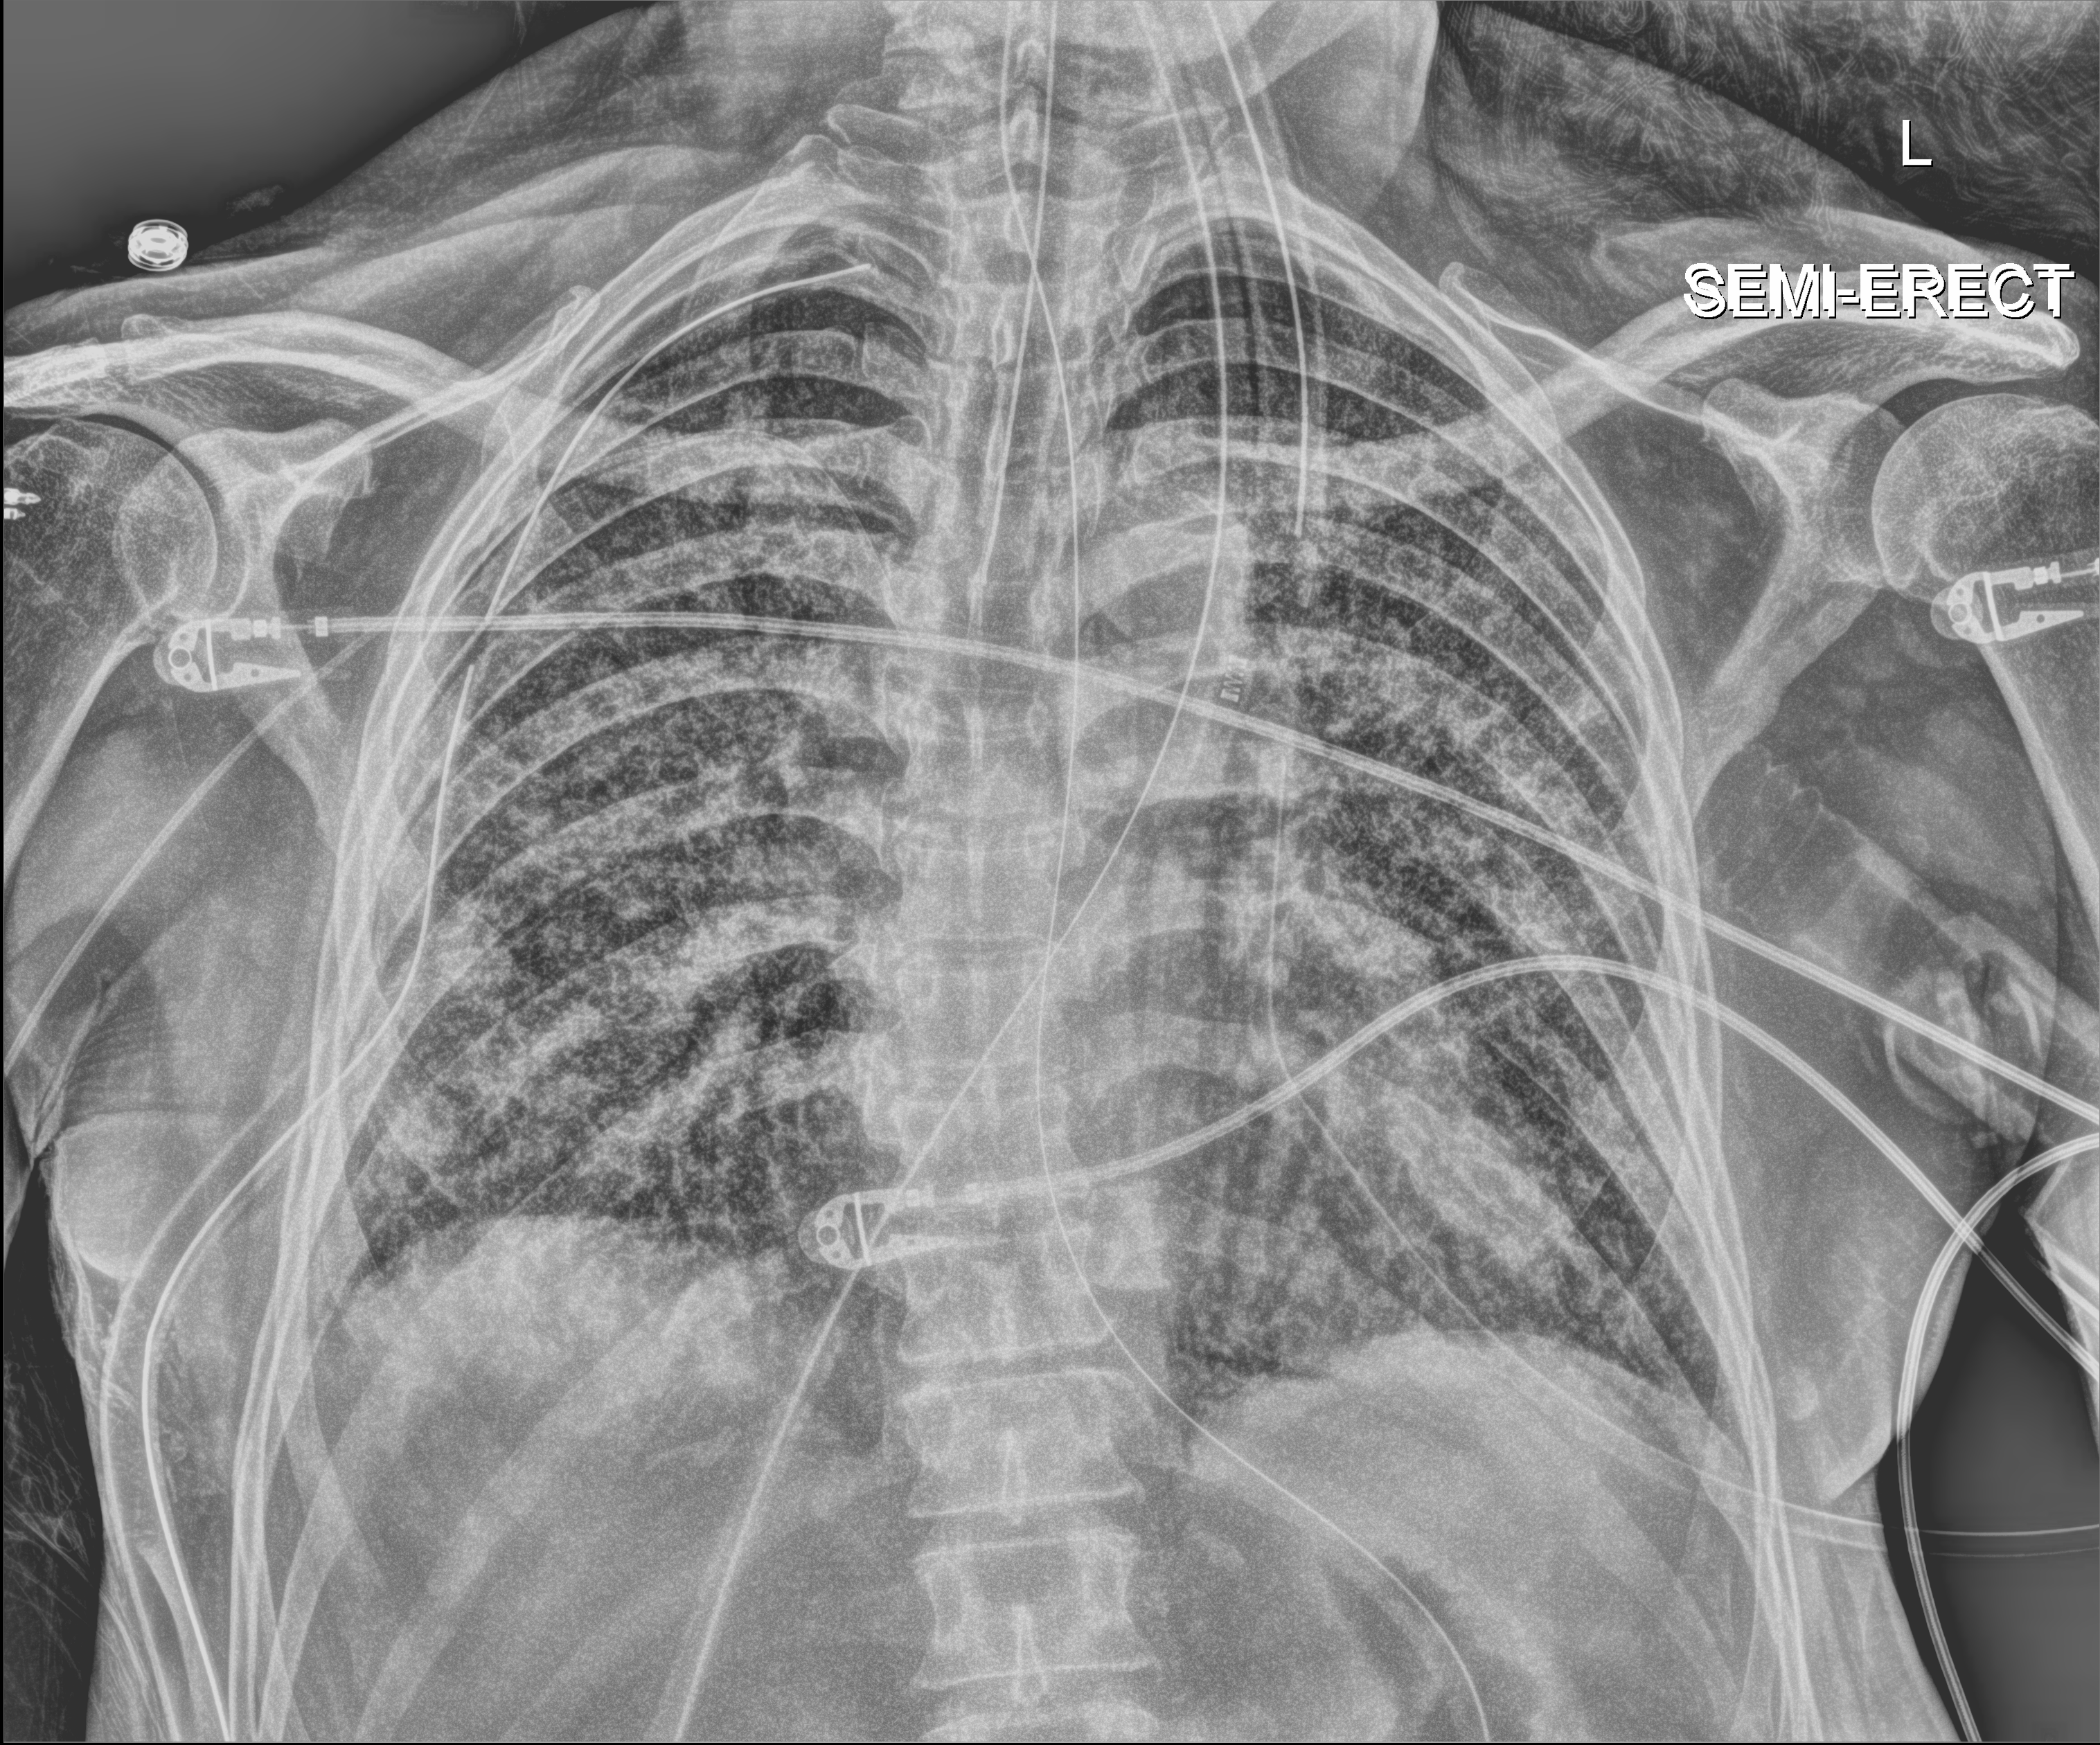
Portable chest radiograph; anteroposterior (AP) projection. Male patient hospitalised with COVID-19, age 60–74 years.
Admission-level facts for this patient (not findings on this image; timing relative to this image not recorded): mechanically ventilated during this hospital stay: yes.